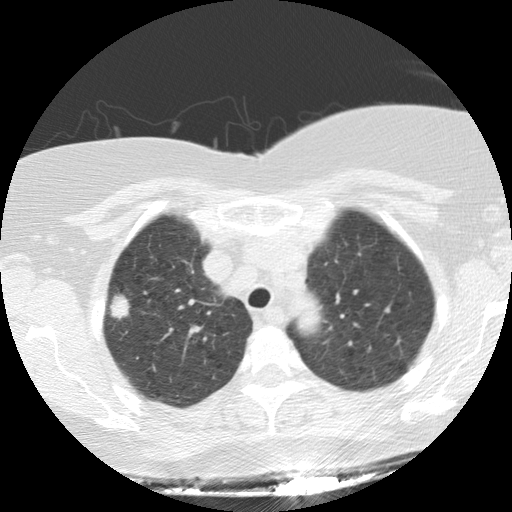
Axial slice from a low-dose chest CT screening exam; first (baseline) screen; lung window (W 1500 / L -600 HU); 2.5 mm slice thickness; standard (soft-tissue) reconstruction kernel (STANDARD); slice 27 of 136 in the series. Female, age 64 years at enrolment. Current smoker at enrolment.
Expert-annotated lung lesion, bounding box [x1, y1, x2, y2] px = [92, 274, 143, 332]. The exam's reader record, not a measurement of the box and not confirmed to be the same lesion: non-calcified nodule or mass ≥4 mm, right upper lobe, 17 × 16 mm, spiculated (stellate) margins, soft tissue attenuation. Participant outcome: lung cancer diagnosed 70 days after this screen — adenocarcinoma, NOS, right upper lobe, stage IIIA (AJCC 6th edition), 15 mm at pathology.